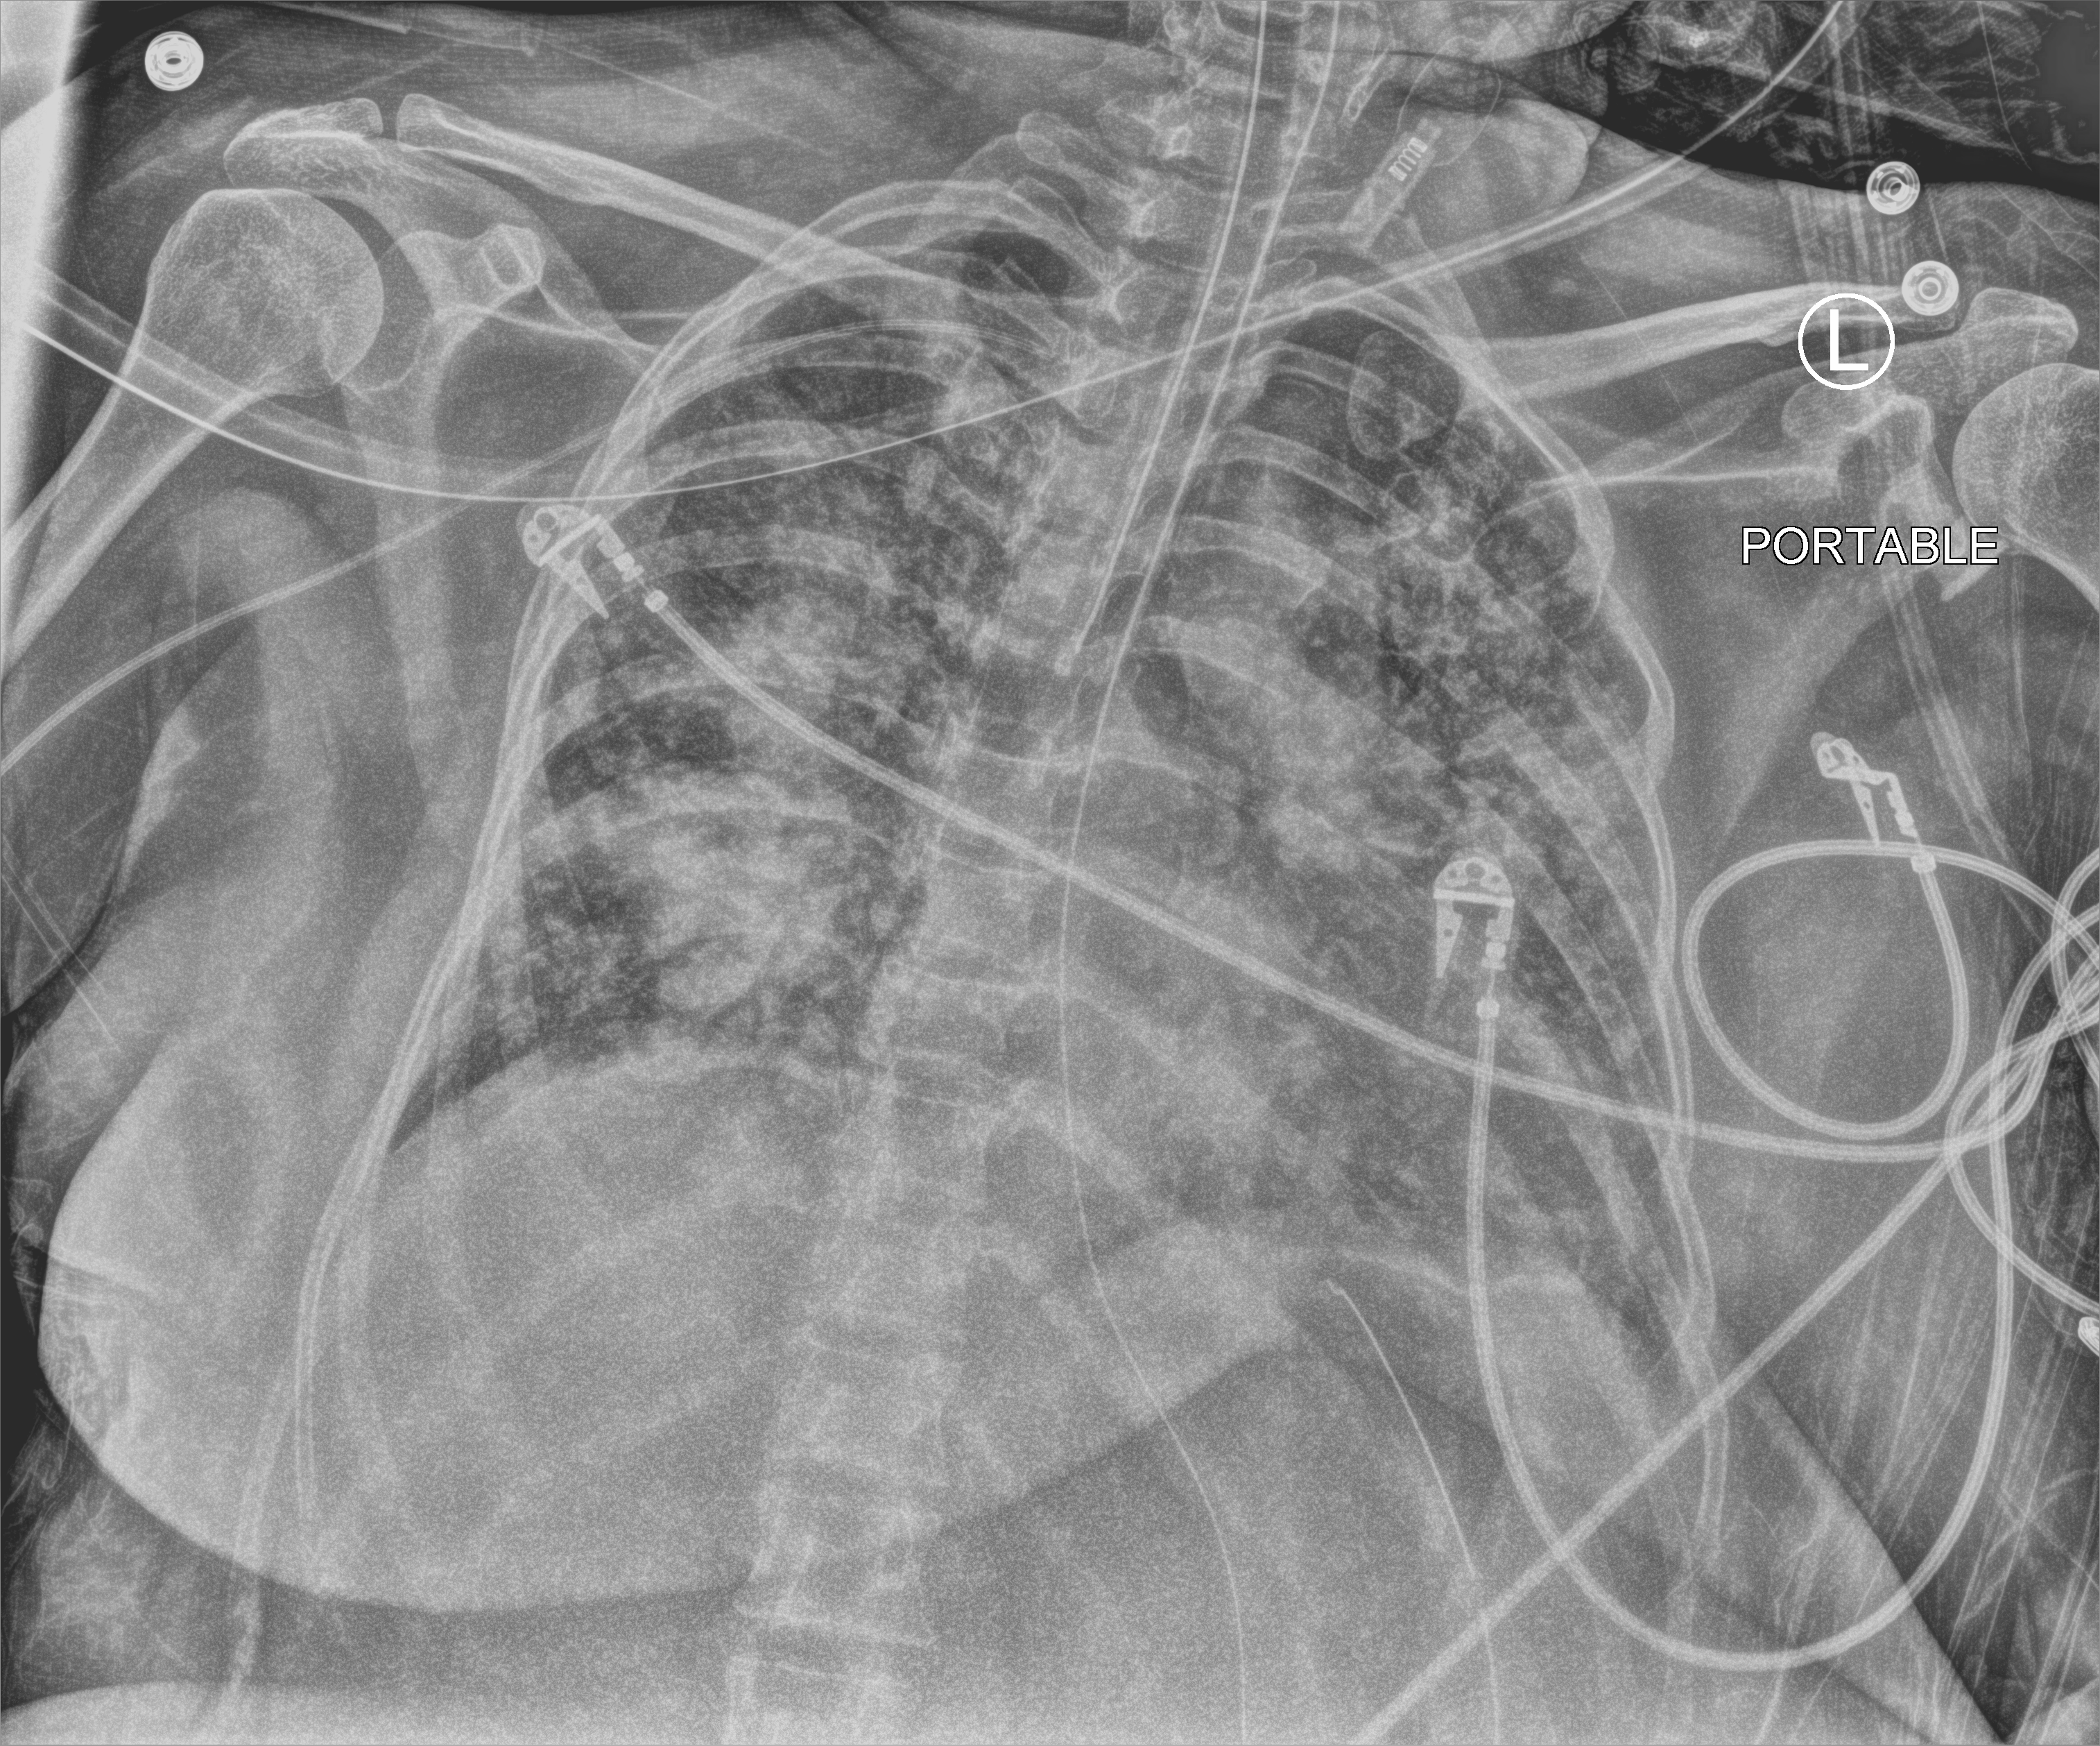
Bedside chest radiograph (computed radiography); anteroposterior (AP) projection. Adult patient hospitalised with COVID-19, age 18–59 years.
From the hospital-stay record, not from the radiograph (when in the stay this image was taken is not recorded):
- hypertension (admission record): no